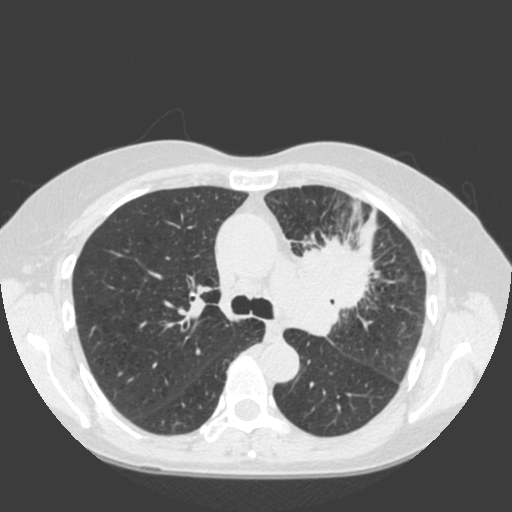
Low-dose screening chest CT, one axial slice; position 126 of 184 along the scan axis; lung window (W 1500 / L -600 HU); 512 × 512 image matrix, field of view 350 × 350 mm.
Outlined on this slice (expert manual segmentation):
- lesion 1 (tumor, hilum of left lung): bounding box <288,198,378,338> (left, top, right, bottom; pixels)